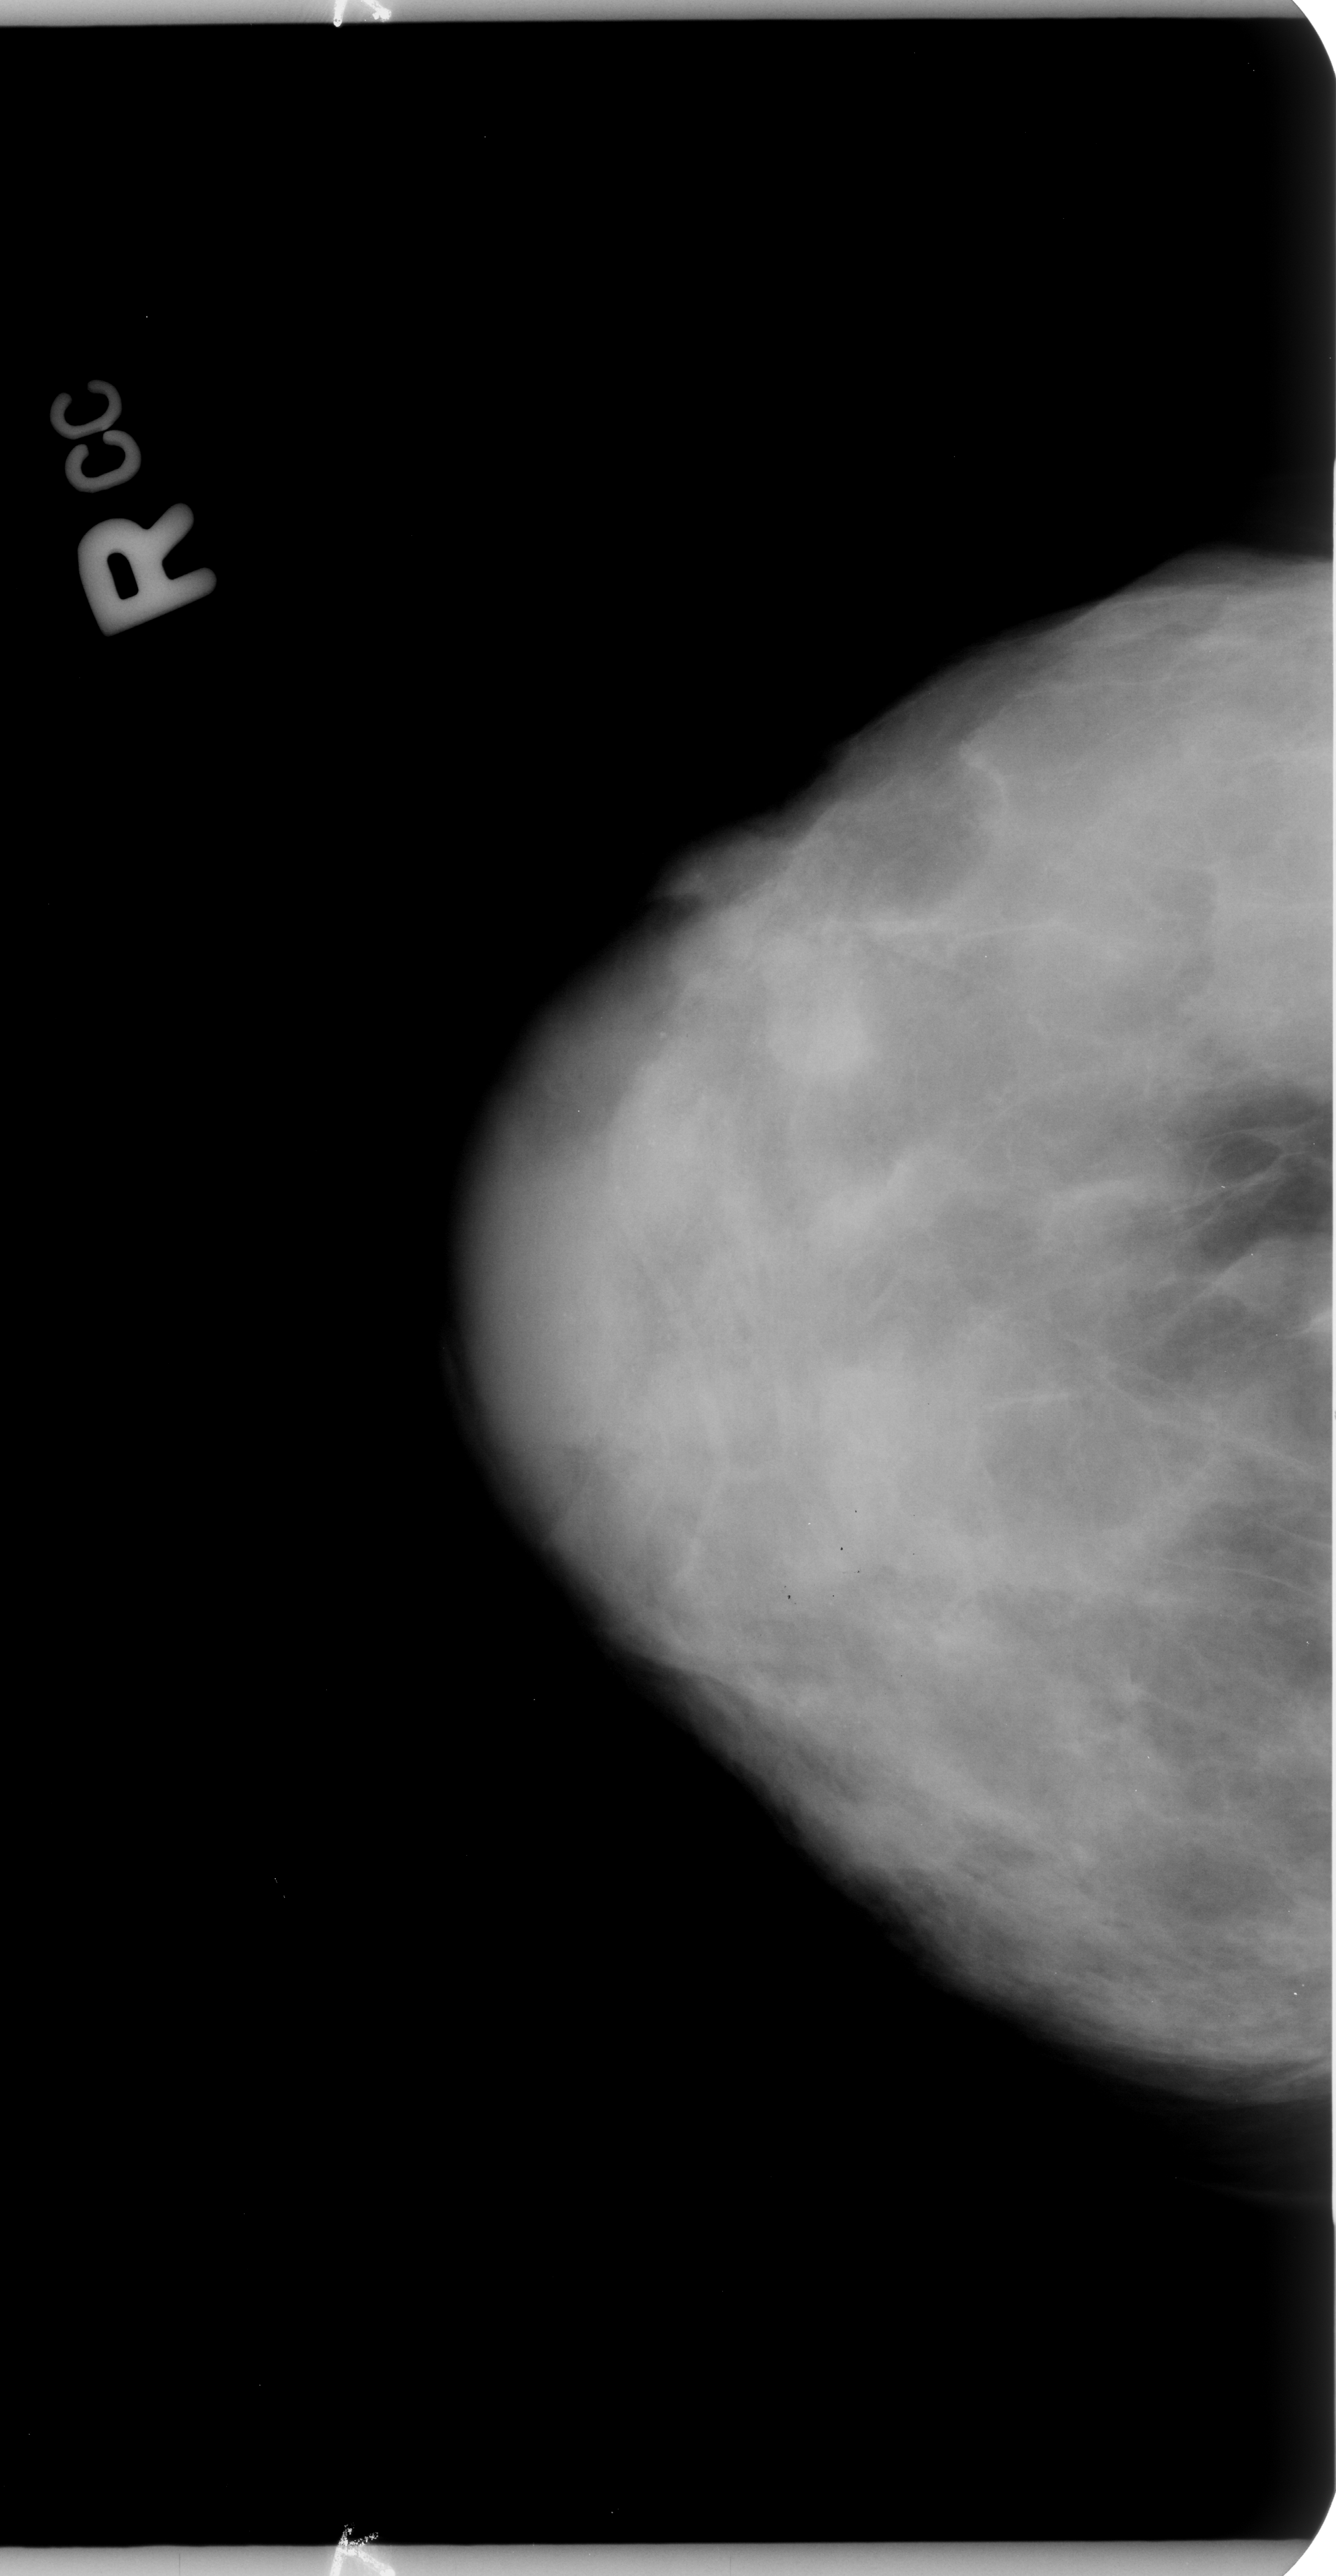
Mammogram (digitized film); right breast; craniocaudal (CC) view; breast composition: extremely dense (BI-RADS density category 4 of 4); 1336 × 2576 image matrix.
Marked abnormalities (boxes around the expert regions of interest):
- calcifications, morphology pleomorphic, distribution regional; BI-RADS assessment category 4; subtlety rating 3 on a 1 (subtle) to 5 (obvious) scale; pathology (as recorded): benign: bounding box [x1, y1, x2, y2] px = [461, 865, 937, 1874]